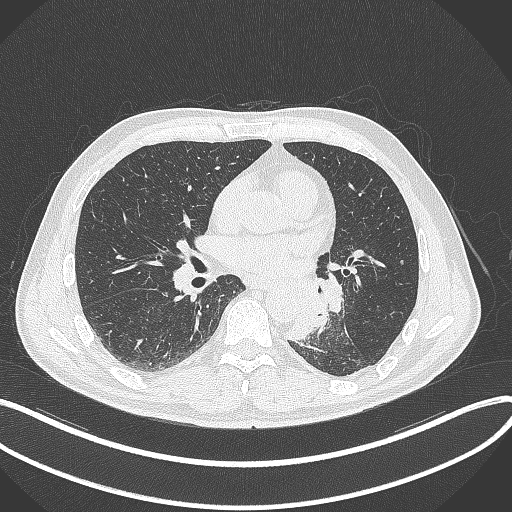
Chest CT, one axial slice; position 159 of 329 along the scan axis; reconstruction kernel B70f; 120 kVp; lung window (W 1500 / L -600 HU); 512 × 512 image matrix, field of view 400 × 400 mm. Patient: male, 59 years. From the clinical record (not read from this slice): clinical TNM (as recorded): T2a N2 M0.
Outlined on this slice (rectangle marked by the reading radiologist):
- lung tumour (recorded histology: squamous cell carcinoma): box from (x=287, y=288) to (x=330, y=341) px